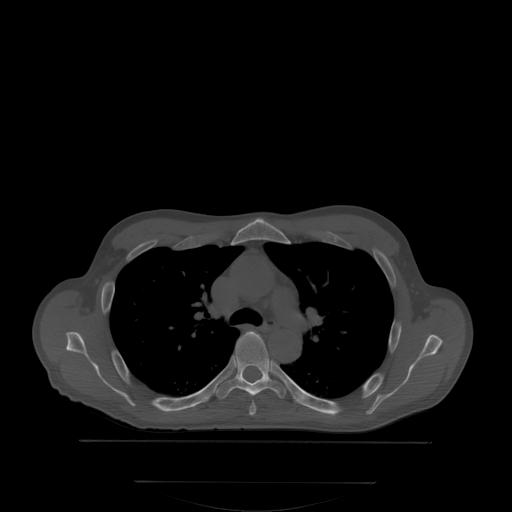
CT including the spine, one axial slice. Position 249 of 350 along the scan axis. Bone window (W 1800 / L 400 HU). 512 × 512 image matrix. Male patient, age 58 years. From the clinical record (not read from this slice): primary cancer: prostate.
Annotated regions visible in this slice (semi-automatically segmented with operator editing):
- T4 vertebra: box from (x=251, y=403) to (x=256, y=414) px
- T5 vertebra: (x=216, y=331)–(x=293, y=398)